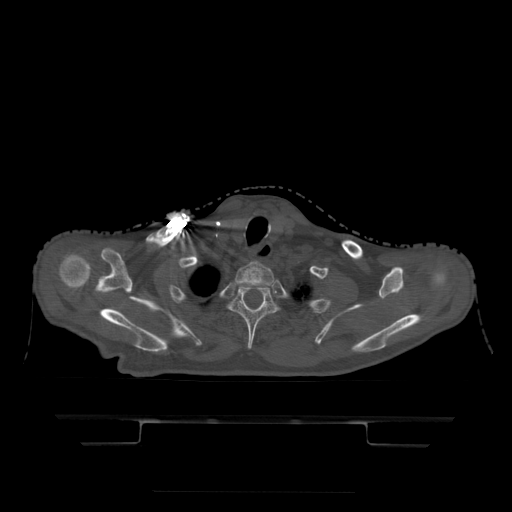
CT including the spine, one axial slice. Bone window (W 1800 / L 400 HU). 1.25 mm slice thickness. 512 × 512 image matrix, field of view 436 × 436 mm. Patient age 68 years. From the clinical record (not read from this slice): primary cancer: urothelial.
Annotated regions visible in this slice (semi-automatic segmentation, software-assisted and operator-edited):
- T1 vertebra: box from (x=235, y=263) to (x=274, y=288) px
- T2 vertebra: (x=229, y=286)–(x=277, y=350)